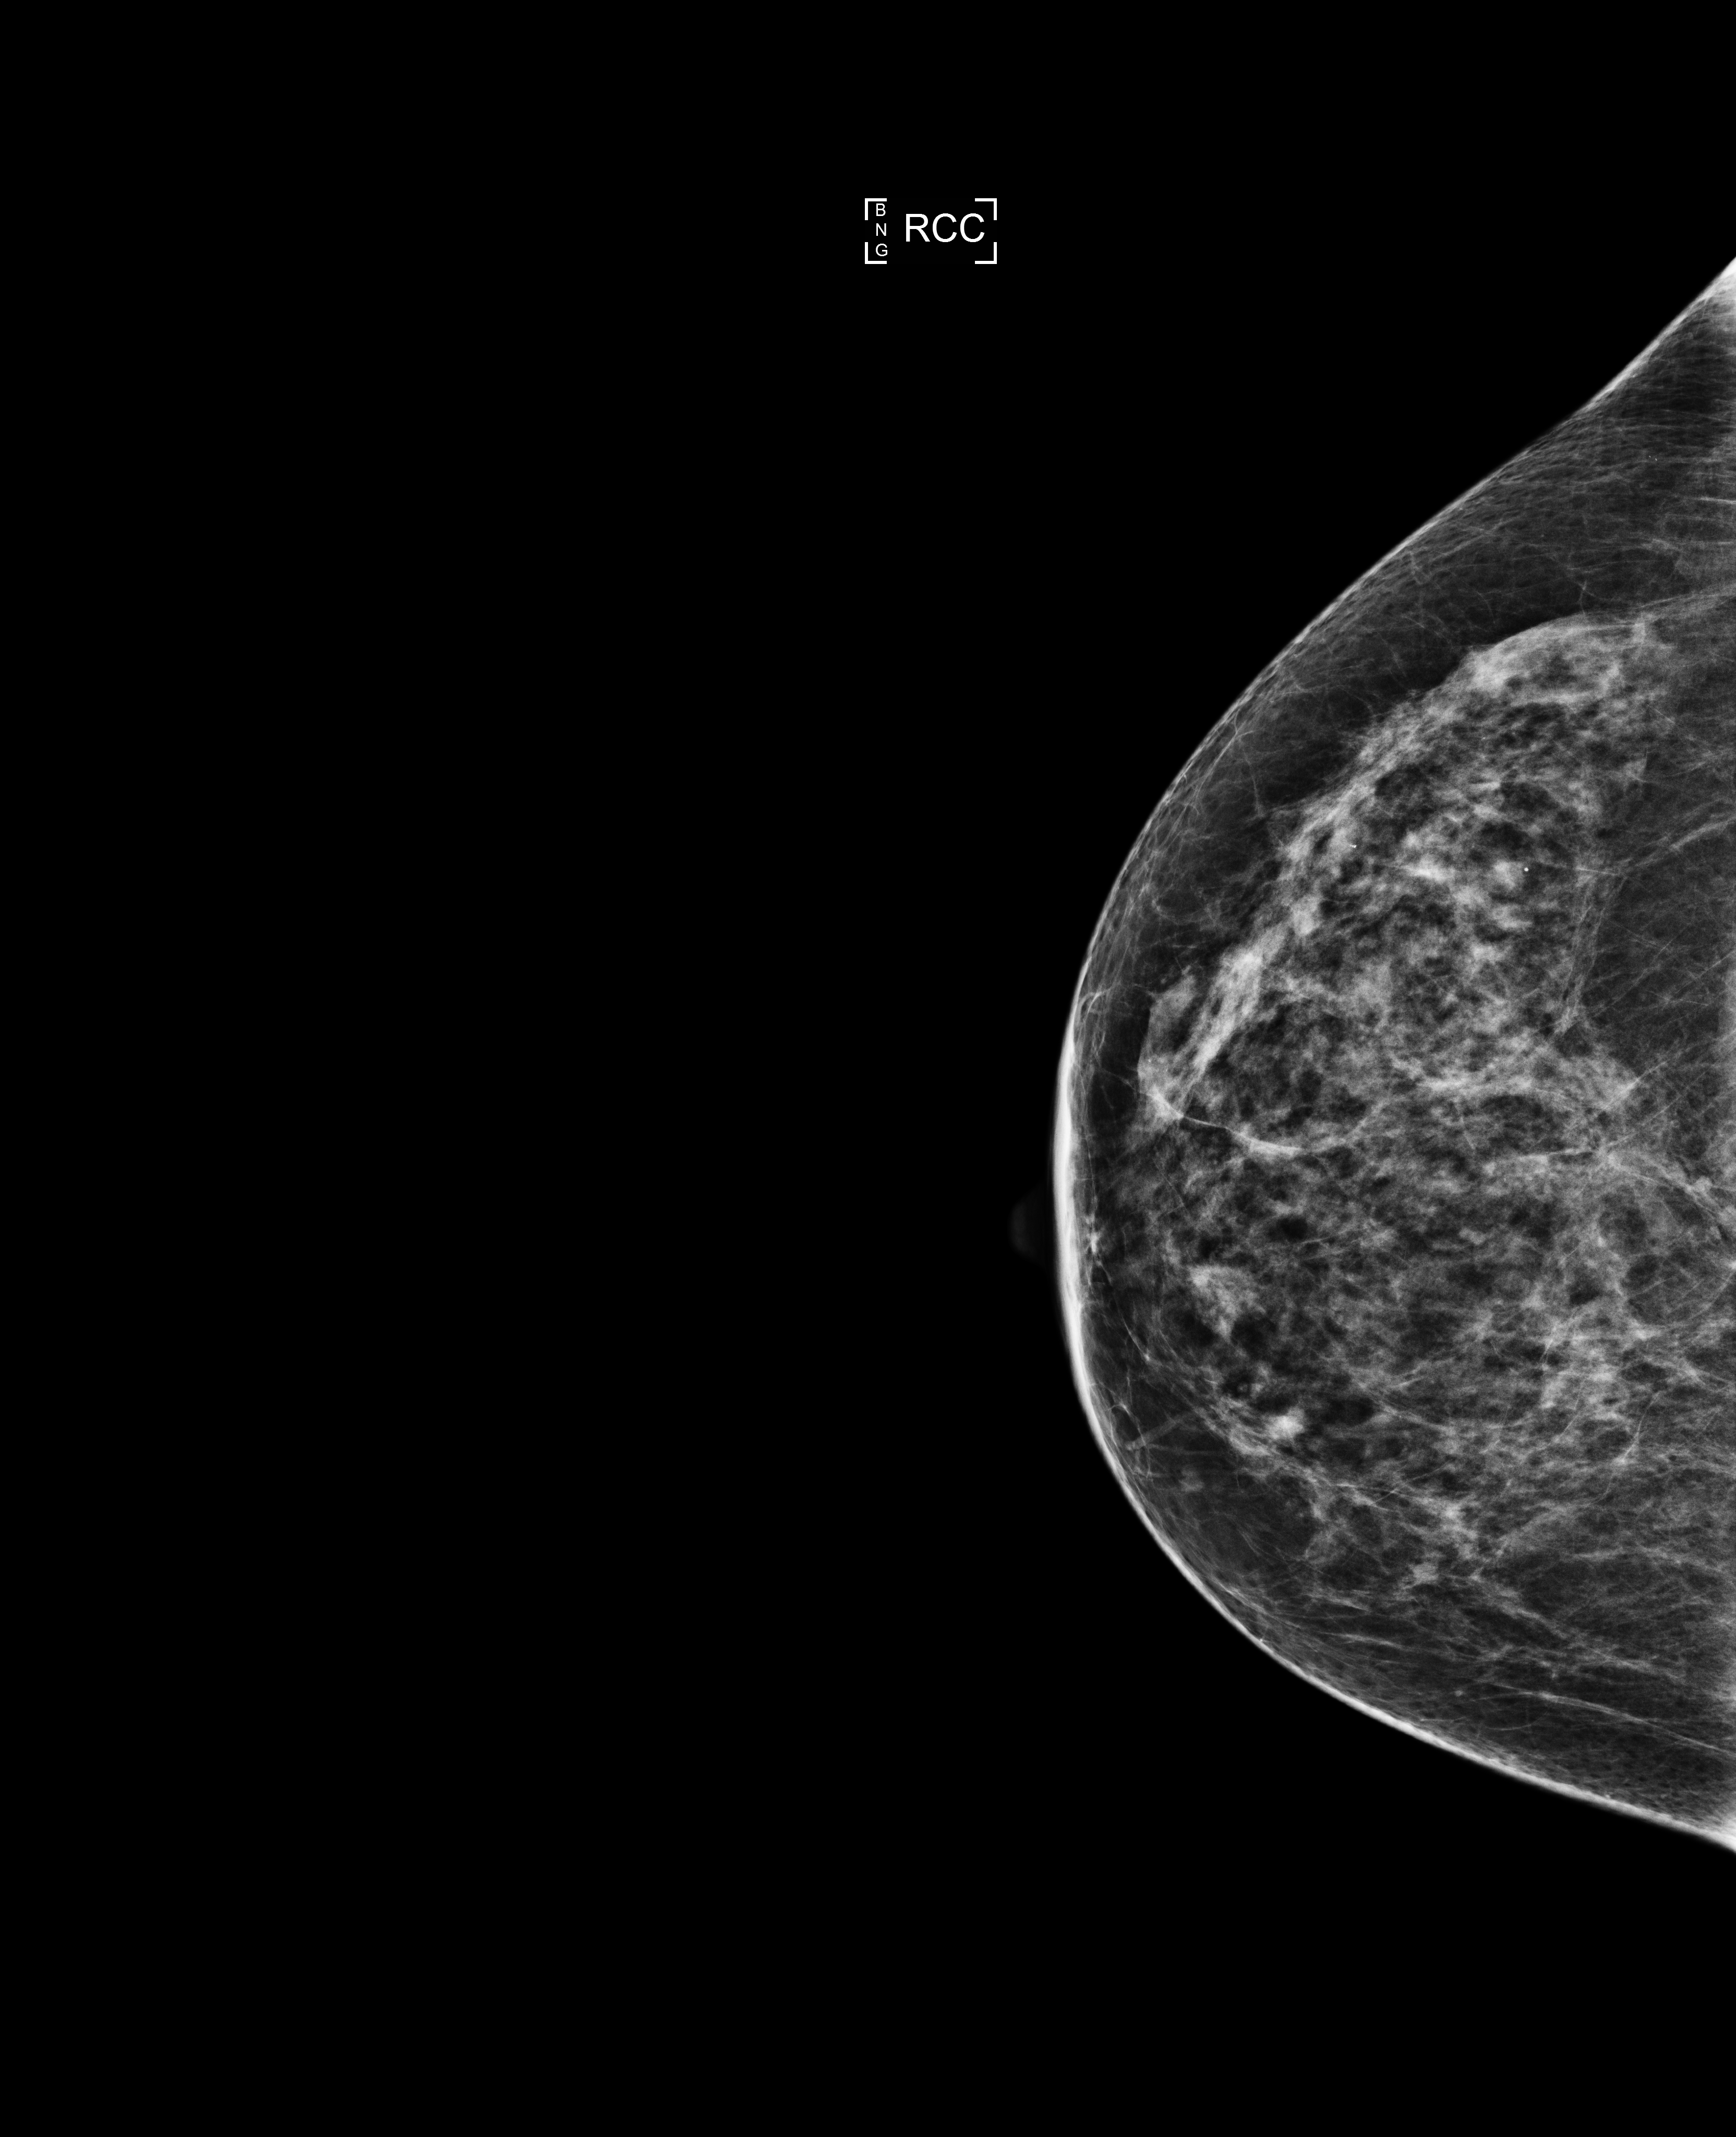
Annual screening mammography examination, compressed breast thickness 61 mm, system: Selenia Dimensions. Female patient, age 62 years.
Image type: full-field digital mammogram. Breast: right. Projection: cranio-caudal projection.